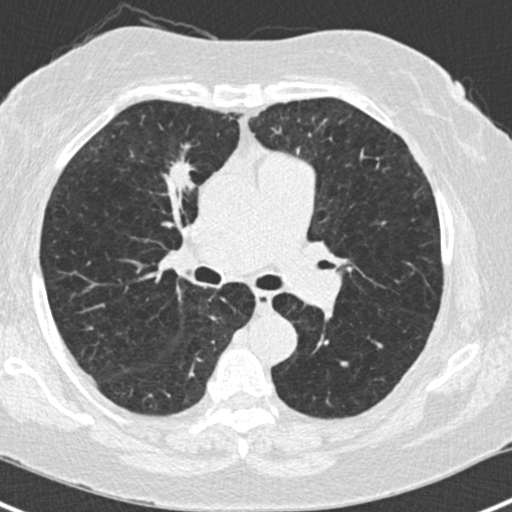
Low-dose screening chest CT, one axial slice. Position 90 of 168 along the scan axis. Reconstruction kernel B30f. 120 kVp. Lung window (W 1500 / L -600 HU). 2 mm slice thickness. 512 × 512 image matrix.
Annotated regions visible in this slice (manually delineated by an expert):
- lesion 1 (tumor, upper lobe of right lung): bounding box [x1, y1, x2, y2] px = [170, 157, 195, 196]